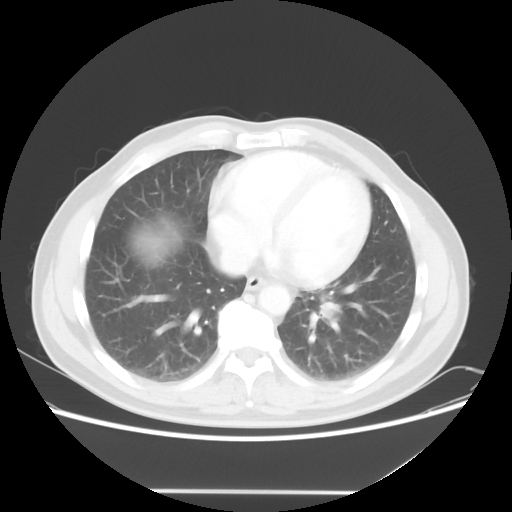
Chest CT, one axial slice; position 20 of 56 along the scan axis; lung window (W 1500 / L -600 HU); 5 mm slice thickness; 512 × 512 image matrix. Patient: male, 61 years. Case-level facts recorded for this patient, not image findings: clinical TNM (as recorded): T1c N0 M0; histopathological grade: G3.
Structures marked on this image (rectangle marked by the reading radiologist):
- lung tumour (recorded histology: adenocarcinoma): bounding box <319,295,342,335> (left, top, right, bottom; pixels)